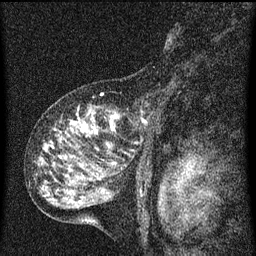
Breast MRI (dynamic contrast-enhanced), one sagittal slice. Slice 36 of 60 in the series (ordered by position). Dynamic contrast-enhanced series, image 2 of 3 at this slice position (ordered by acquisition). 1.5 T. TE 4.2 ms, TR 8 ms. 2 mm slice thickness. 256 × 256 image matrix, field of view 180 × 180 mm. Female patient, age 55 years.
Structures marked on this image (semi-automatic segmentation, software-assisted and operator-edited):
- analysis volume of interest (the breast-tissue region the enhancement analysis was run in; not a lesion): bounding box [x1, y1, x2, y2] px = [40, 94, 157, 159]
- tumour enhancement mask (voxels above the 70 % enhancement threshold inside the analysis volume of interest): [72, 114, 117, 145]